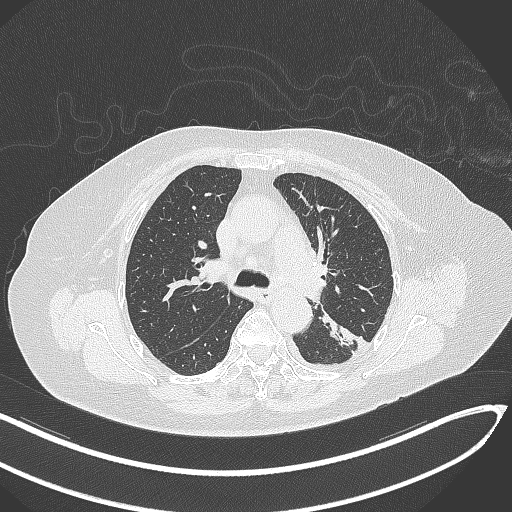
Chest CT, one axial slice; slice 207 of 270 in the series (ordered by position); reconstruction kernel B70f; 120 kVp; lung window (W 1500 / L -600 HU); 512 × 512 image matrix, field of view 400 × 400 mm. Patient: female, 76 years. Case-level facts recorded for this patient, not image findings: clinical TNM (as recorded): T1c N0 M0.
Annotated regions visible in this slice (rectangle marked by the reading radiologist):
- lung tumour (recorded histology: adenocarcinoma): bounding box (x1, y1, x2, y2) in pixels: (315, 302, 366, 354)